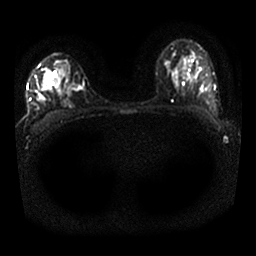
Breast MRI, one axial slice. Diffusion-weighted series; image 2 of 4 stored at this slice position (different b-values; order by instance number). 1.5 T. 256 × 256 image matrix, field of view 330 × 330 mm. Female patient.
Annotated regions visible in this slice (manually delineated by an expert):
- tumour on diffusion-weighted imaging: box from (x=76, y=86) to (x=84, y=92) px